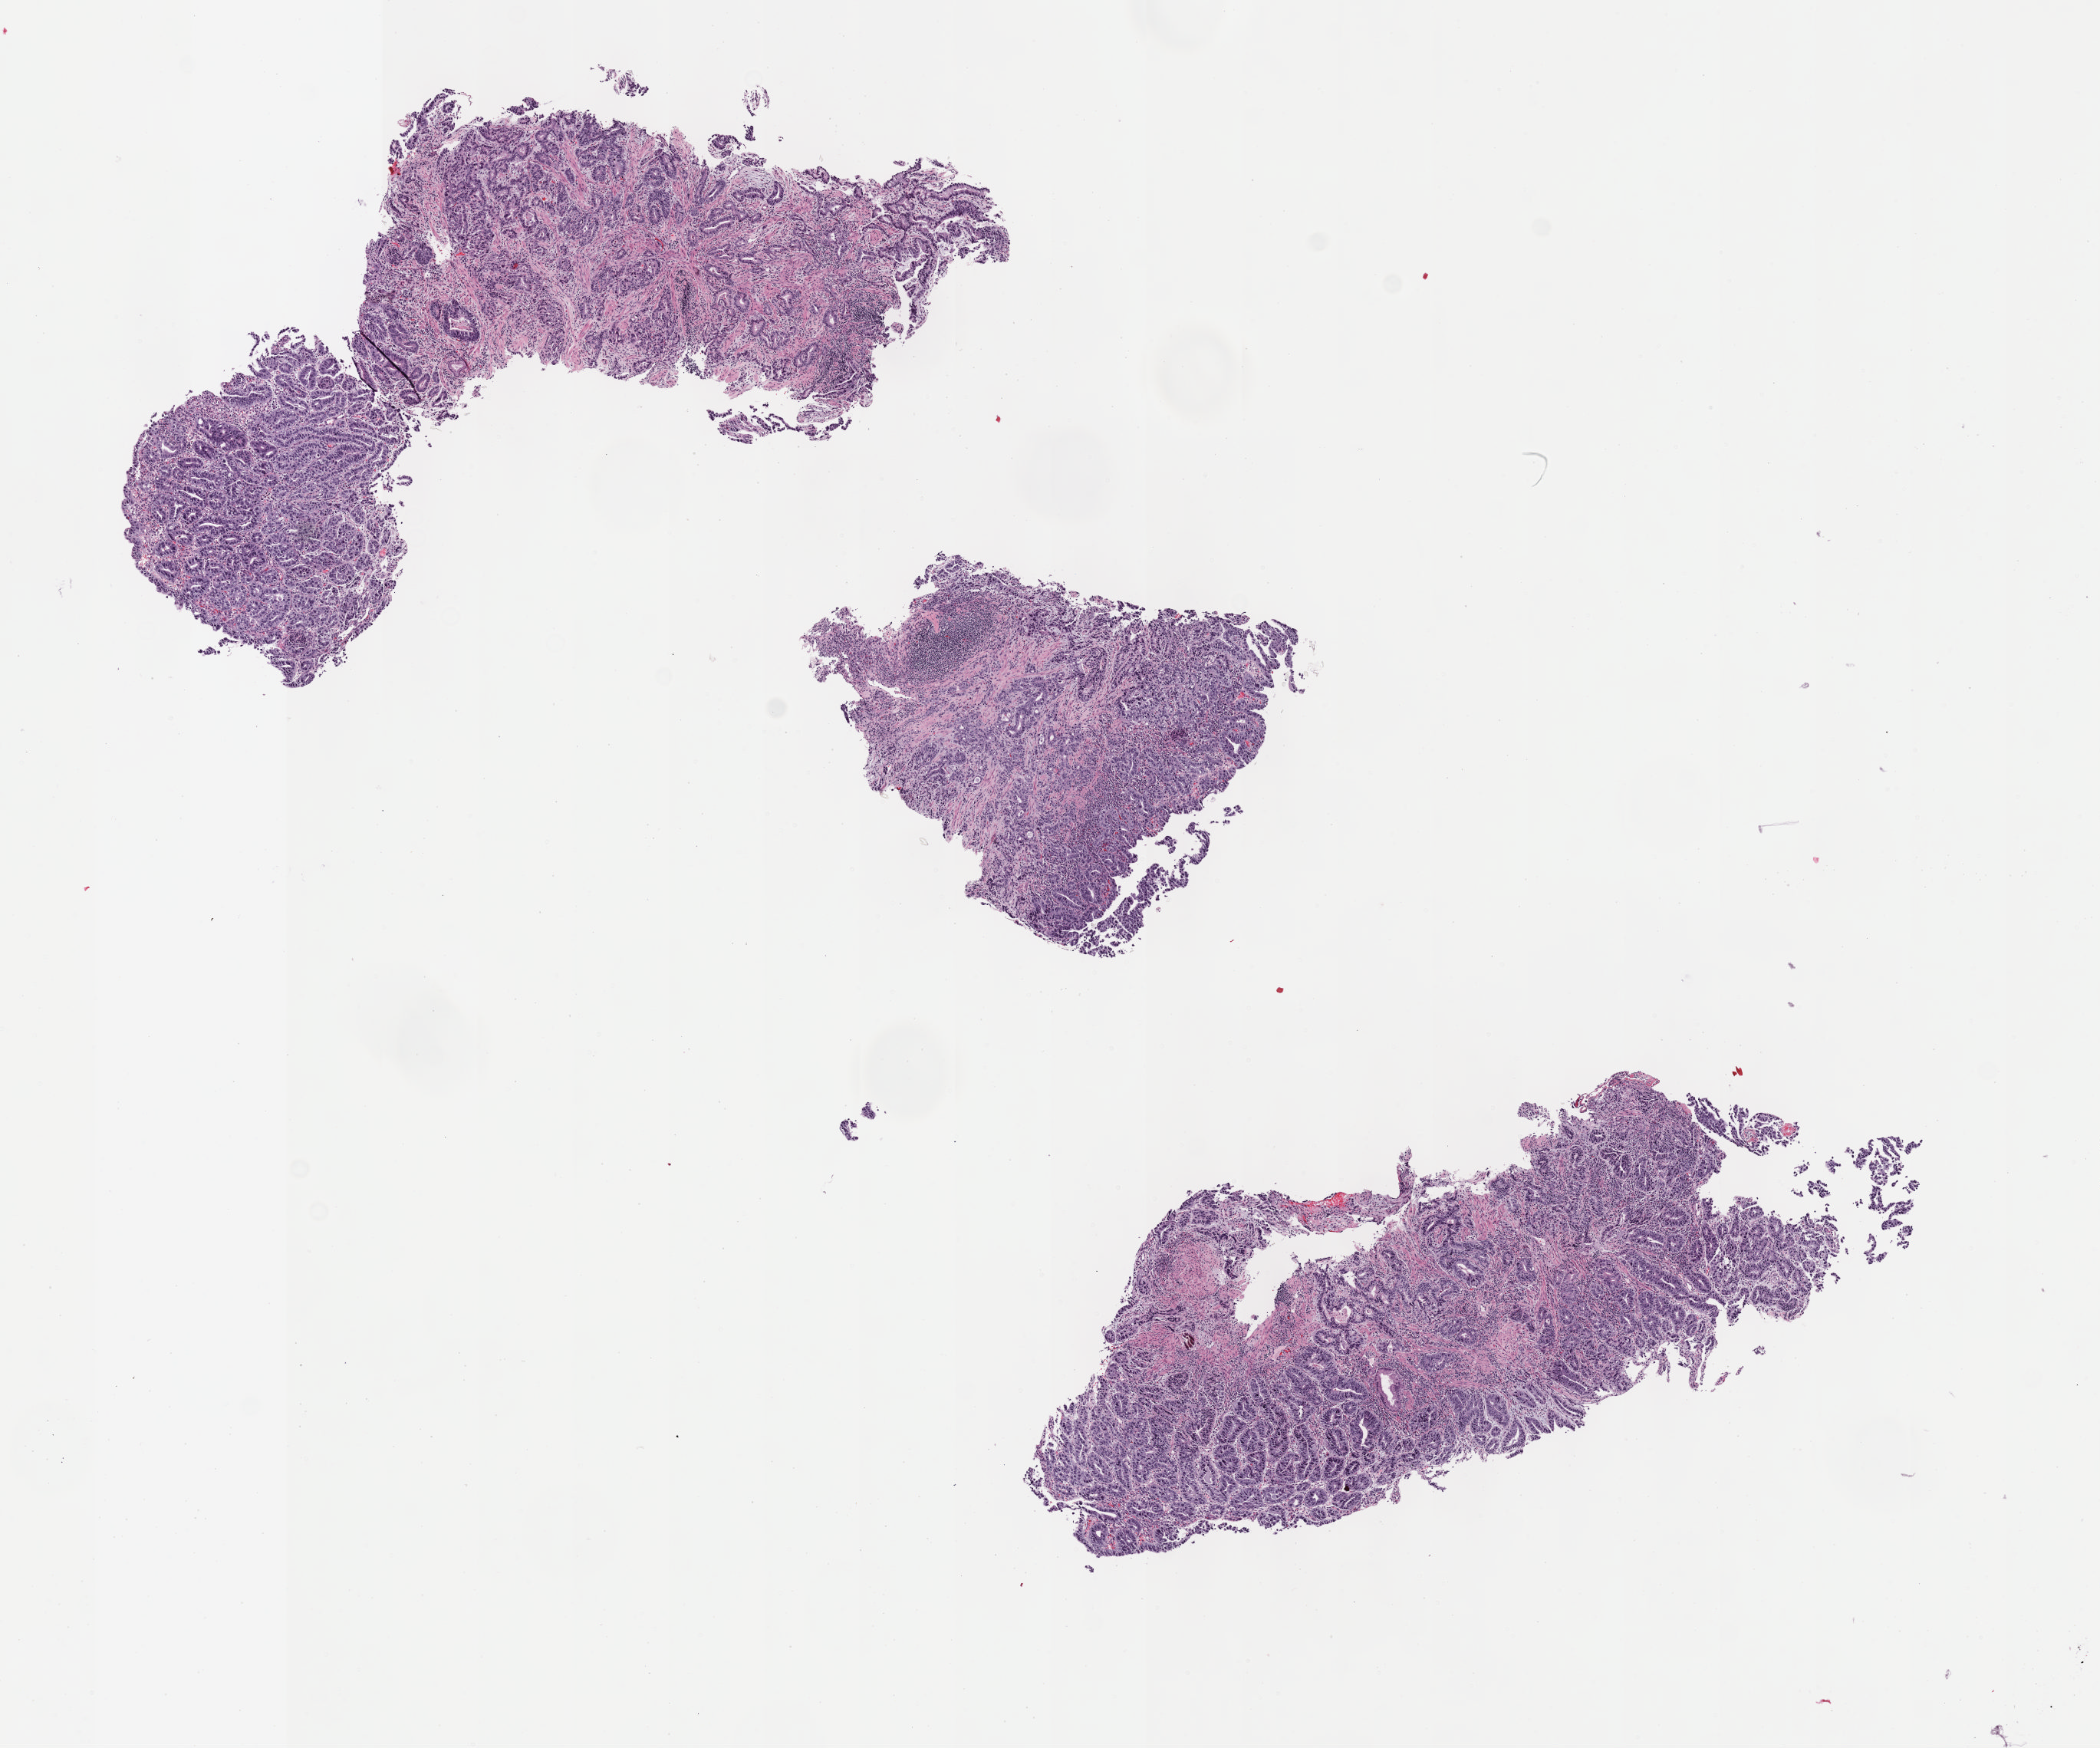
Whole-slide histology image, Hematoxylin and eosin (H&E) stained, a low-resolution overview of the entire scanned area, about 11.1 x 9.2 mm (acquisition: 40x scan); formalin-fixed paraffin-embedded (FFPE) diagnostic section; primary tumour sample from the stomach. Male, age 61 years at initial diagnosis. Histologic grade: G2 (moderately differentiated).
TNM: T2 NX MX. AJCC pathologic stage: IIA (7th edition). Diagnosis: Adenocarcinoma, NOS.